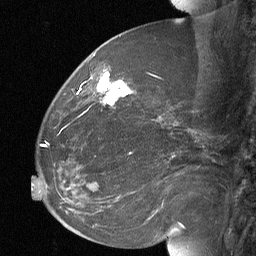
Breast MRI (dynamic contrast-enhanced), one sagittal slice. Position 27 of 64 along the scan axis. Dynamic contrast-enhanced study with each time point stored as its own series, time point 2 of 3 at this slice position (early post-contrast, ordered by acquisition time). 1.5 T. TE 4.8 ms, TR 27 ms. 2 mm slice thickness. 256 × 256 image matrix, field of view 200 × 200 mm. Patient: female, 60 years. From the clinical record (not read from this slice): setting: breast cancer imaged before/during neoadjuvant chemotherapy; receptor status: HR-positive, HER2-negative.
Annotated regions visible in this slice (semi-automatic segmentation, software-assisted and operator-edited):
- analysis volume of interest (the breast-tissue region the enhancement analysis was run in; not a lesion): box from (x=92, y=70) to (x=134, y=109) px
- tumour enhancement mask (voxels above the 90 % enhancement threshold inside the analysis volume of interest): (x=97, y=72)–(x=131, y=105)